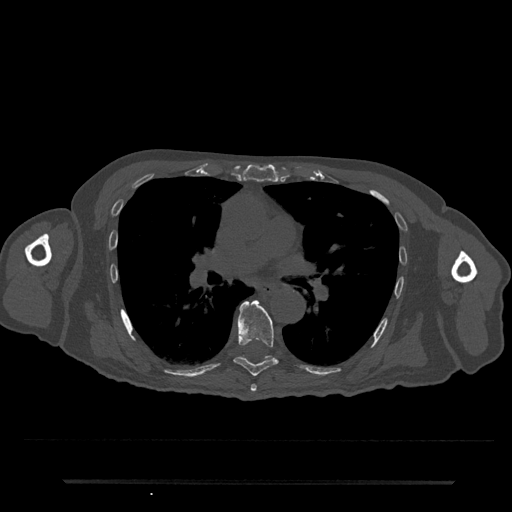
CT including the spine, one axial slice. Slice 475 of 797 in the series (ordered by position). Reconstruction kernel Br40s/3. 120 kVp. Bone window (W 1800 / L 400 HU). 0.5 mm slice thickness. 512 × 512 image matrix, field of view 427 × 427 mm. Male patient, age 74 years. From the clinical record (not read from this slice): primary cancer: prostate.
Annotated regions visible in this slice (semi-automatic segmentation, software-assisted and operator-edited):
- T6 vertebra: bounding box <250,385,257,392> (left, top, right, bottom; pixels)
- T7 vertebra: <233,300,279,377>
- T8 vertebra: <243,356,274,361>